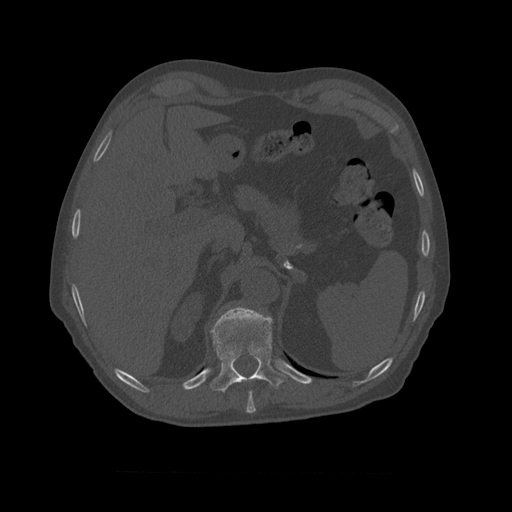
CT including the spine, one axial slice; slice 403 of 450 in the series (ordered by position); reconstruction kernel STANDARD; 120 kVp; bone window (W 1800 / L 400 HU); 1.25 mm slice thickness; 512 × 512 image matrix, field of view 405 × 405 mm. Patient age 75 years. From the clinical record (not read from this slice): primary cancer: prostate.
Outlined on this slice (semi-automatically segmented with operator editing):
- T10 vertebra: bounding box [x1, y1, x2, y2] px = [210, 307, 287, 393]
- T11 vertebra: [227, 306, 240, 307]
- T9 vertebra: [247, 391, 256, 411]